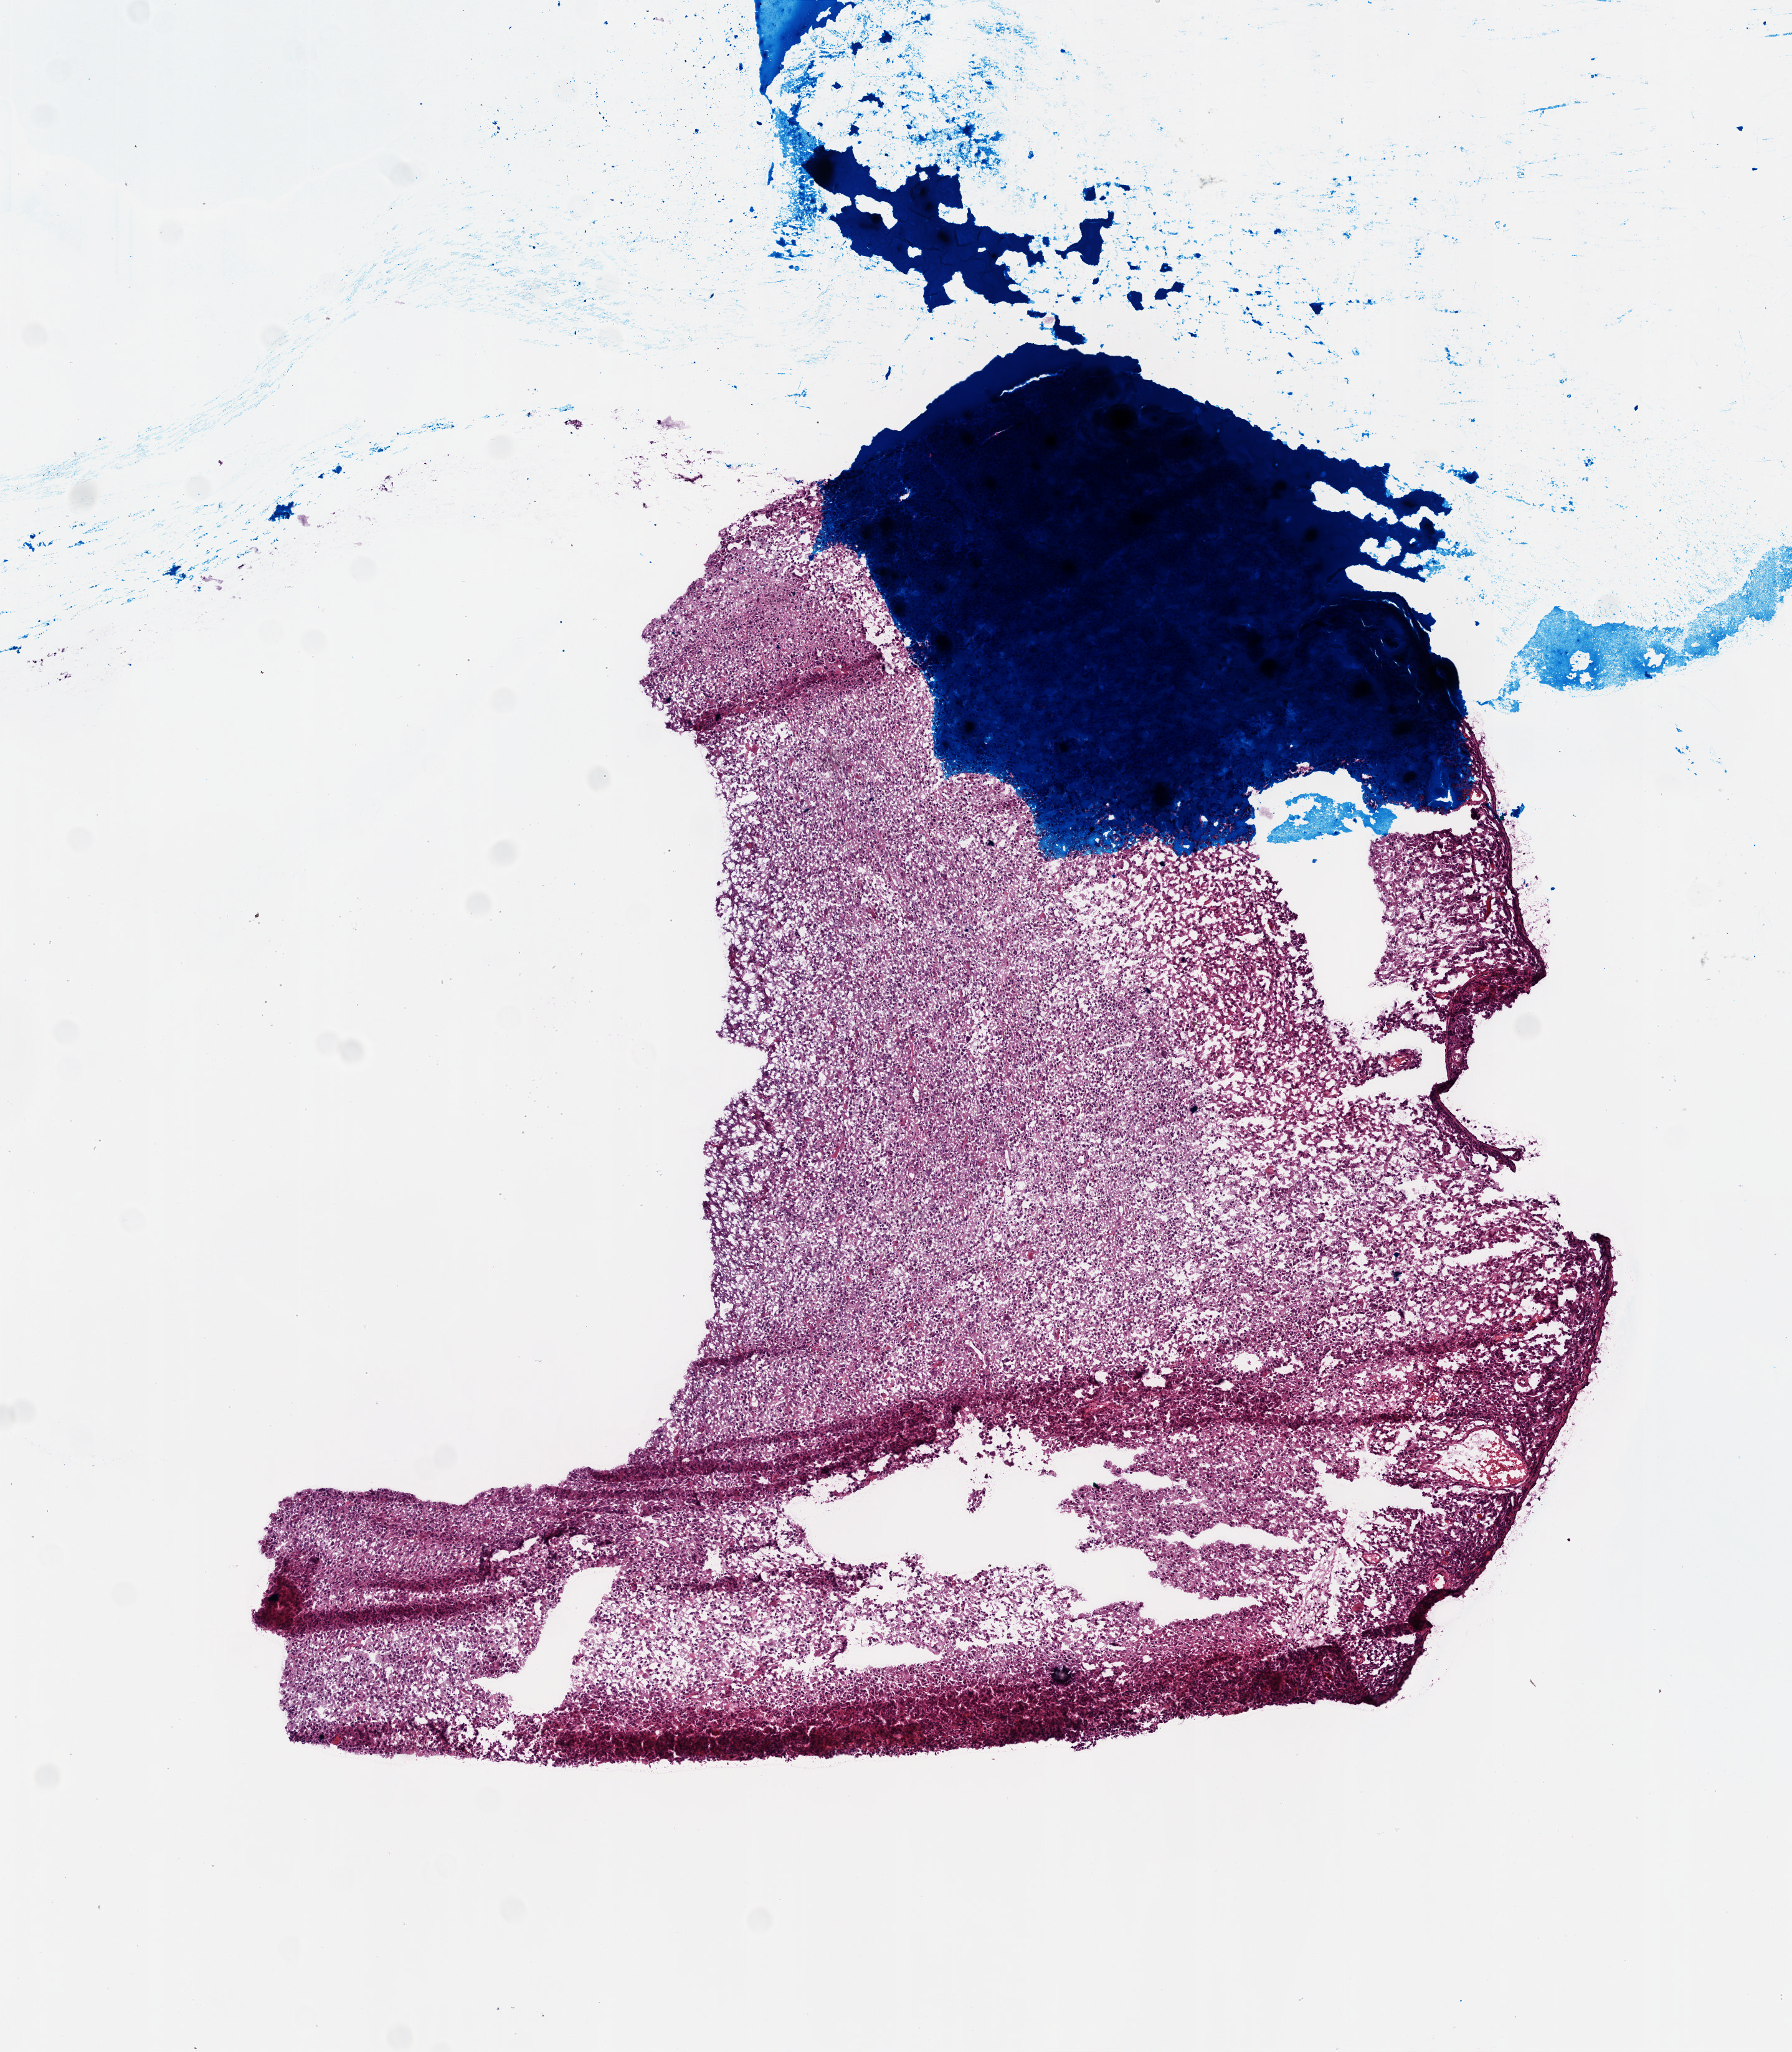
Hematoxylin and eosin (H&E) stained whole-slide image, whole scanned area (about 5.8 x 6.6 mm, slide scanned at 20x) shown as a low-resolution overview; frozen section; primary tumour sample from the brain. Patient: male, age at initial diagnosis 17 years. Slide review estimates, as recorded: tumour cells 85%, tumour nuclei 95%, normal cells 0%, stromal cells 5%, necrosis 10%.
Pathologic diagnosis: Glioblastoma.